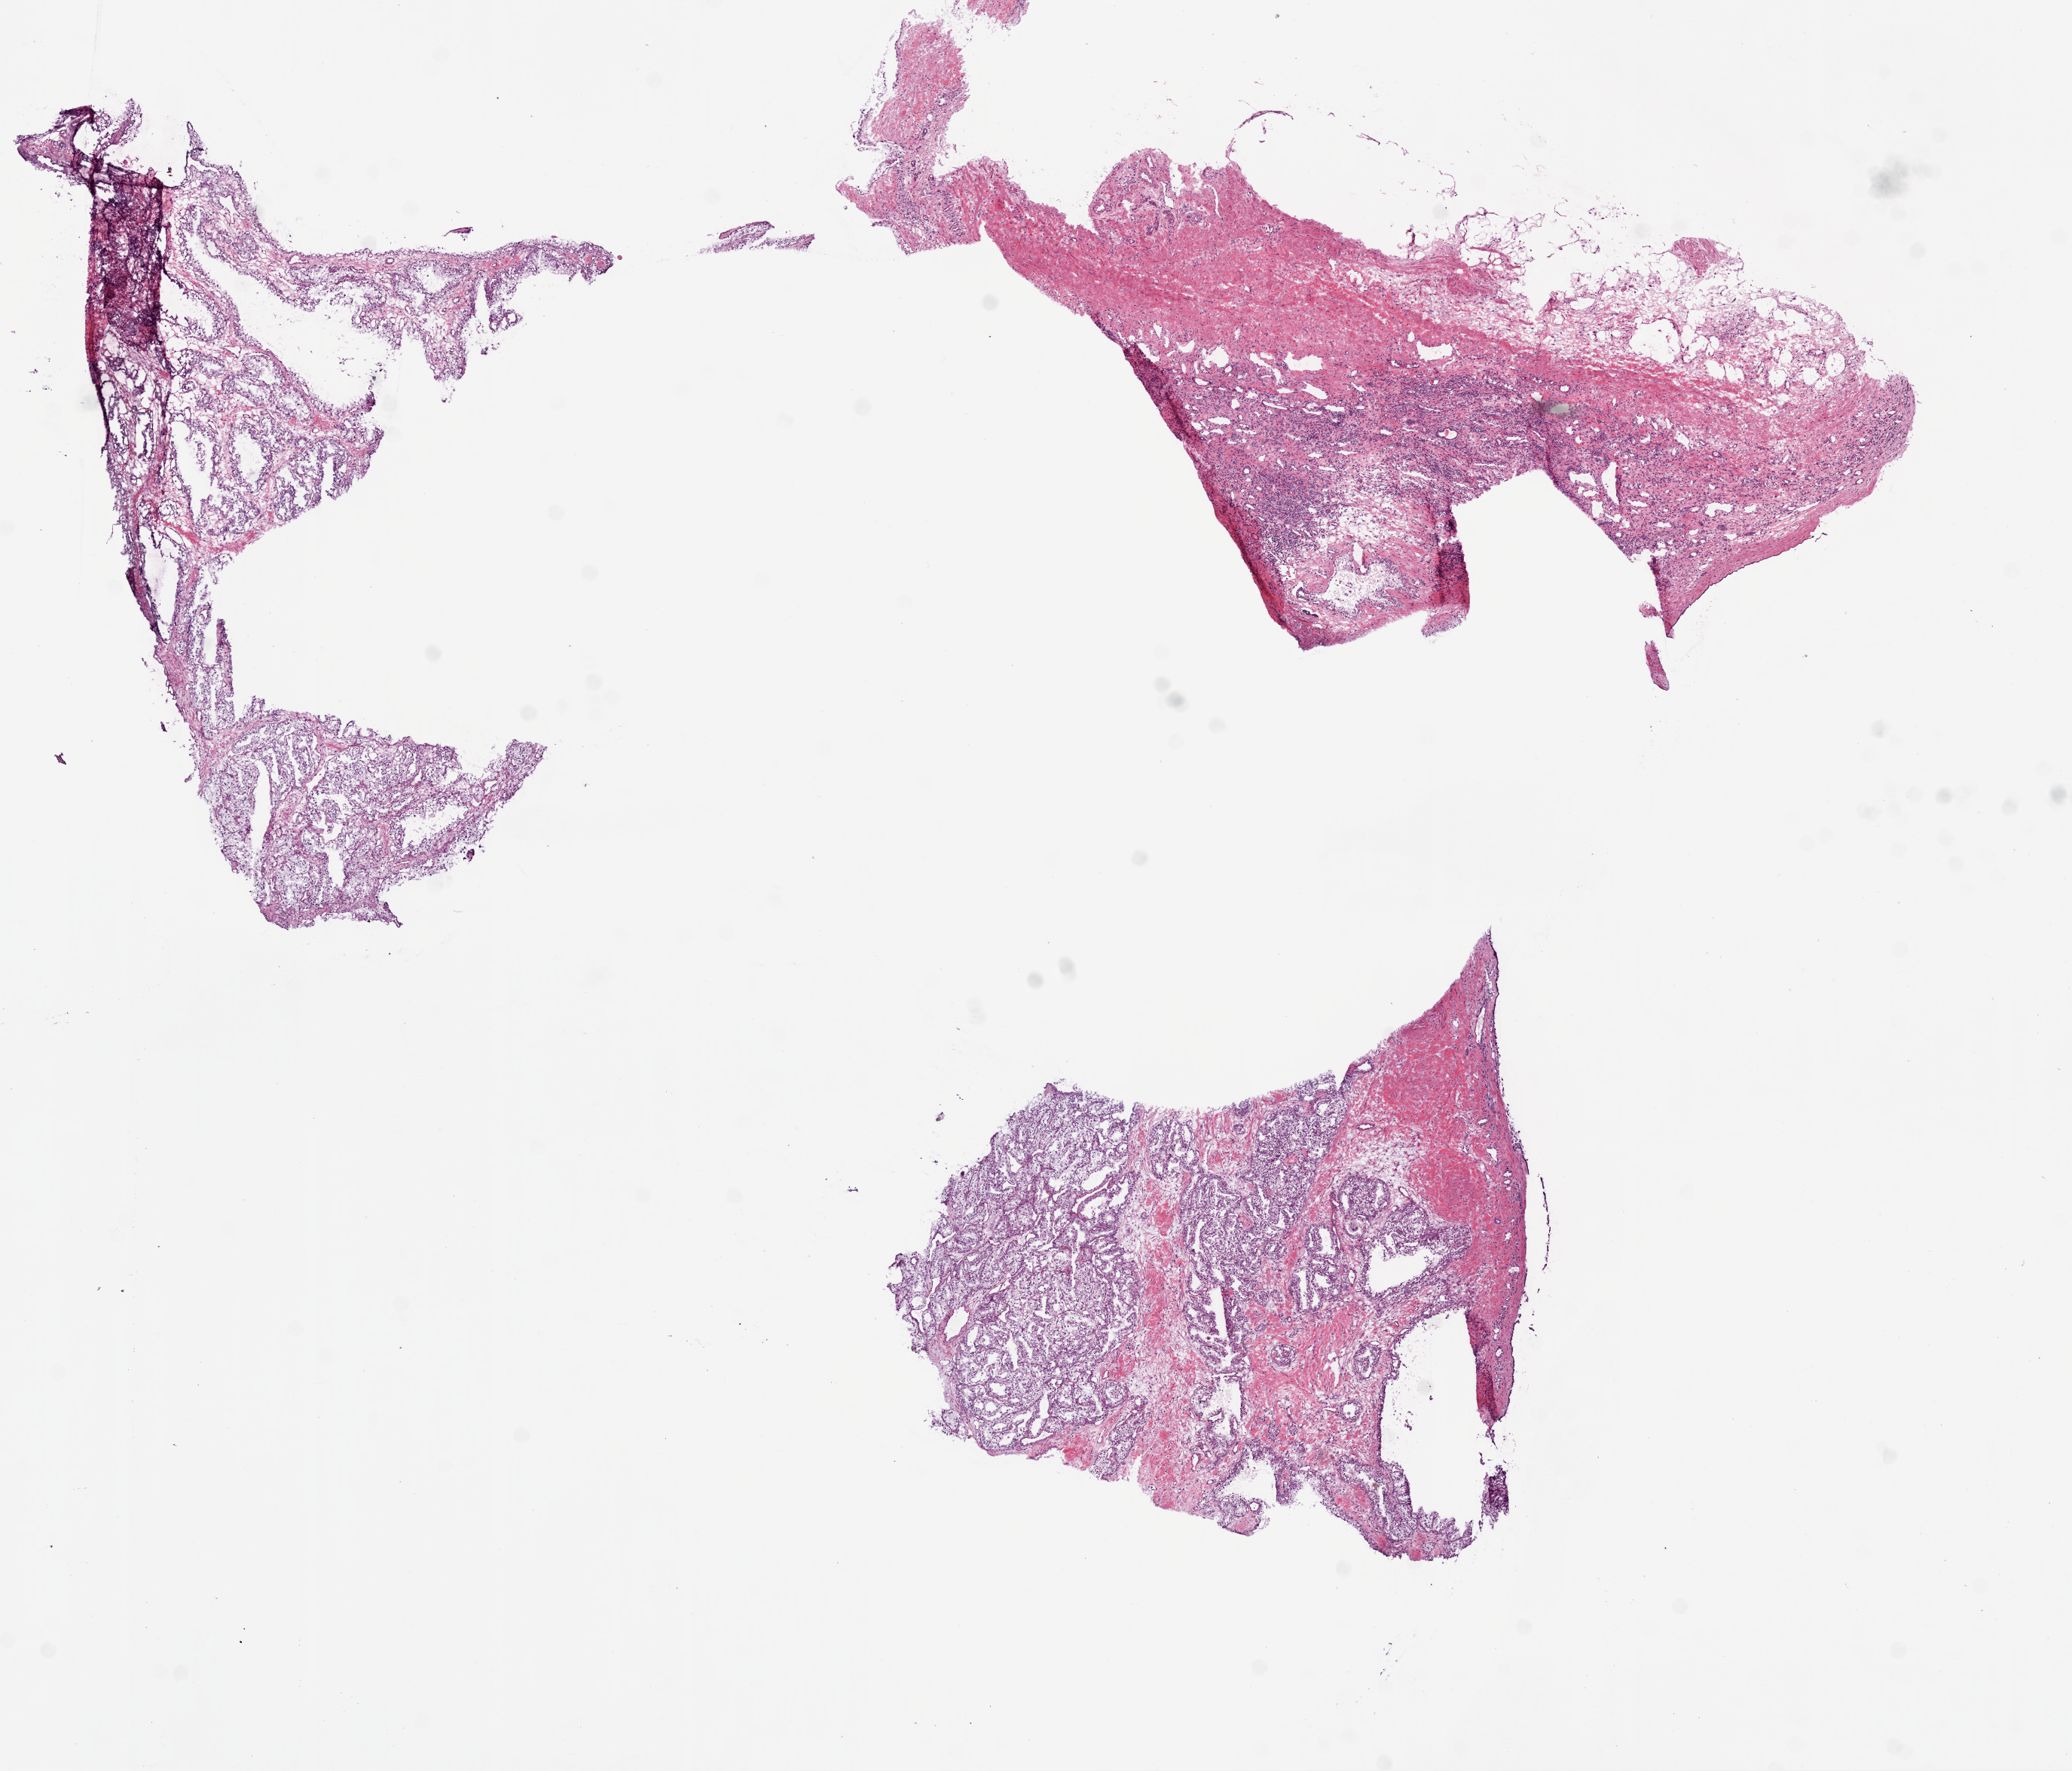
Whole-slide histology image, H&E-stained, shown as a low-resolution overview of the whole scanned area (about 11.0 x 9.4 mm), frozen section from the bottom of the tissue portion, kidney, primary tumour sample. Patient: female, age at initial diagnosis 74 years. Composition of this section per pathologist review: tumour cells 85%, tumour nuclei 75%.
Diagnosis: Clear cell adenocarcinoma, NOS.